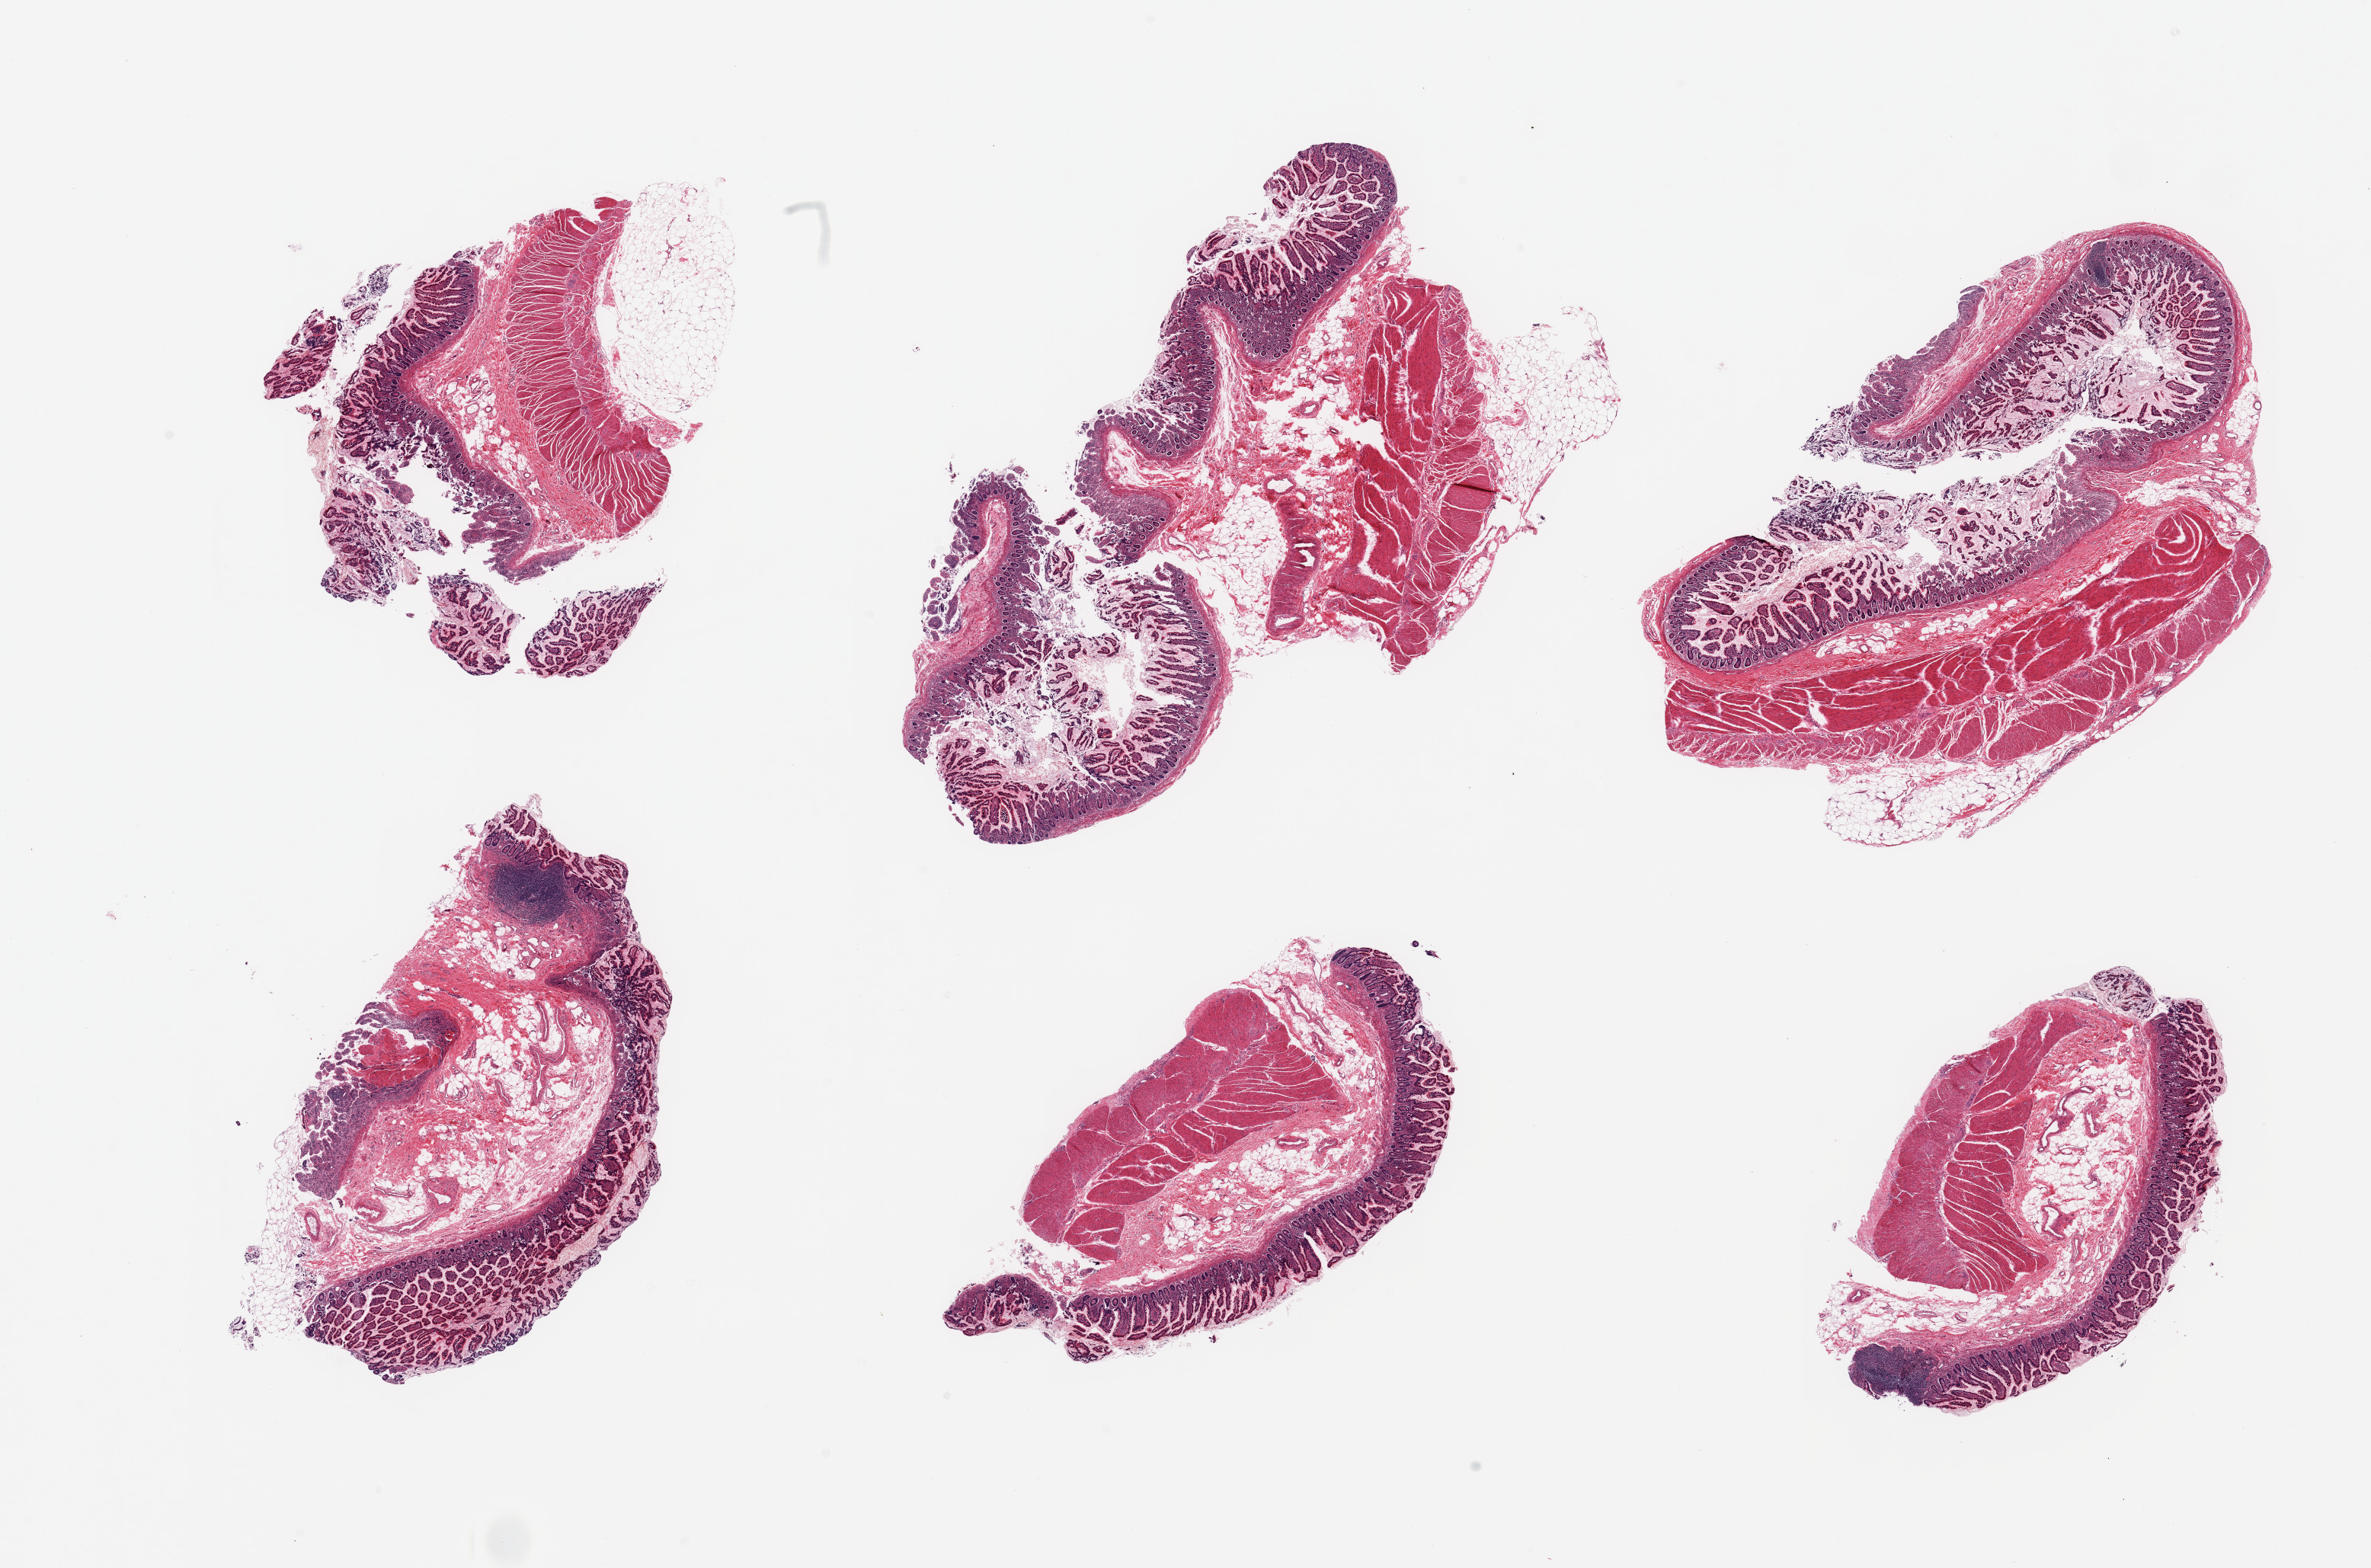
Whole-slide image, hematoxylin and eosin (H&E) stain, shown as a low-resolution overview of the whole scanned area (about 24.6 x 16.3 mm, from a 20x scan). PAXgene-fixed paraffin-embedded (PFPE) section. Sampled site (target tissue): ileum. Tissue donor sample. Donor sex: male.
Review note (as recorded): 6 pieces, correct target but insufficient target lymphoid aggregates for analysis.